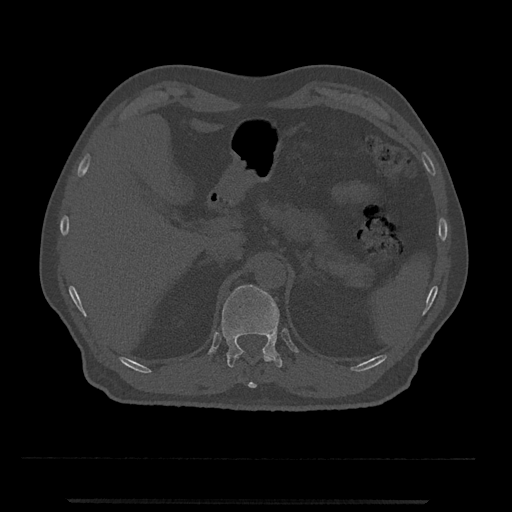
CT including the spine, one axial slice; position 424 of 797 along the scan axis; reconstruction kernel Br40s/3; 120 kVp; bone window (W 1800 / L 400 HU); 0.5 mm slice thickness; 512 × 512 image matrix. Male patient, age 63 years. Case-level facts recorded for this patient, not image findings: primary cancer: prostate.
Annotated regions visible in this slice (semi-automatically segmented with operator editing):
- T11 vertebra: bounding box <235,351,273,388> (left, top, right, bottom; pixels)
- T12 vertebra: <221,285,283,368>